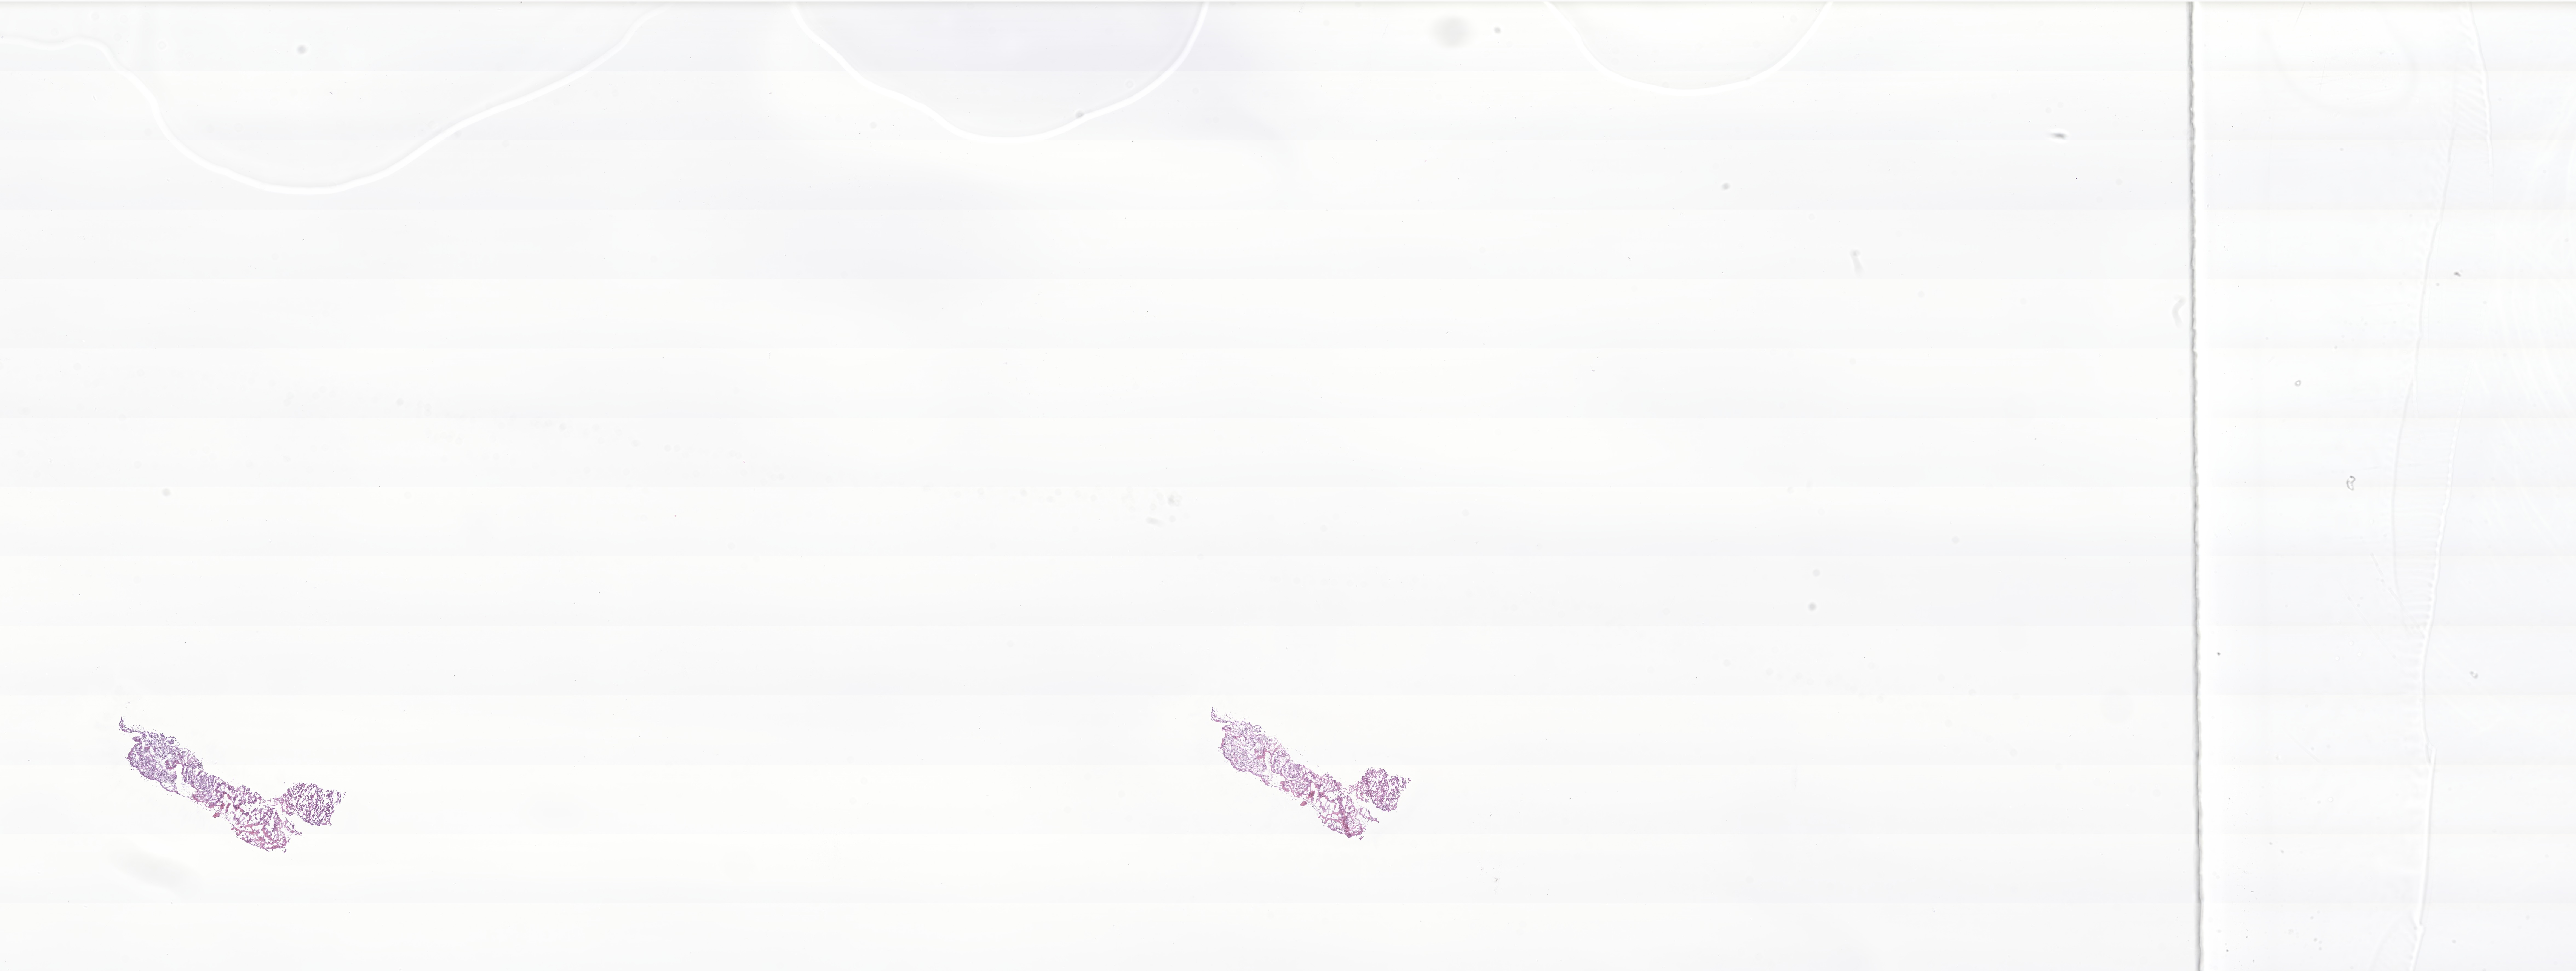
H&E whole-slide image of tumor tissue from the frontal lobe, low-resolution overview of the scanned area, about 39.7 x 14.9 mm, cryosection (OCT / tissue freezing medium). Patient female; age 217 months (18 years 1 month).
Diagnosis (ICD-O-3 morphology term): Glioma, malignant.